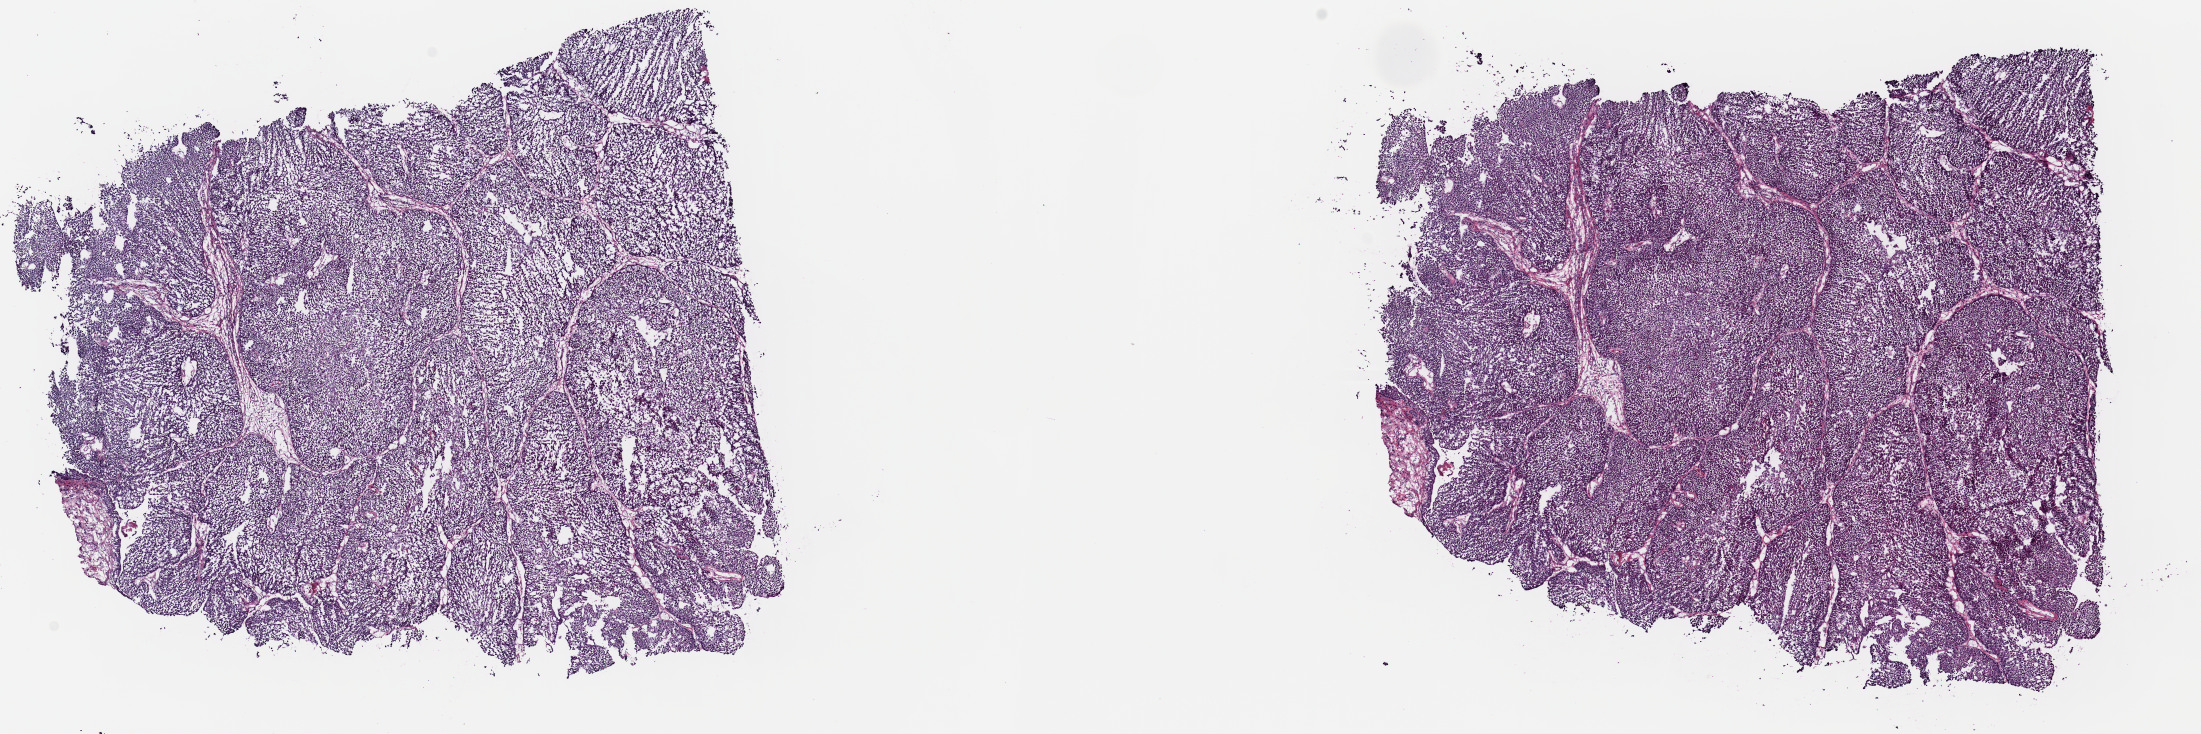
Whole-slide histology image, H&E — whole scanned area (about 17.4 x 5.8 mm, acquisition: 40x scan) shown as a low-resolution overview; frozen section from the top of the tissue portion; sample: primary tumour, bladder. Male patient; age at initial diagnosis 52 years. Histologic grade: high grade. Pathologist review of this section (percent, as recorded): tumour cells 84%, tumour nuclei 95%, normal cells 0%, stromal cells 12%, necrosis 4%. Inflammatory infiltration, as recorded: lymphocyte infiltration 1%, monocyte infiltration 0%, neutrophil infiltration 1%.
• AJCC pathologic stage: III (6th edition)
• histologic diagnosis: Papillary transitional cell carcinoma